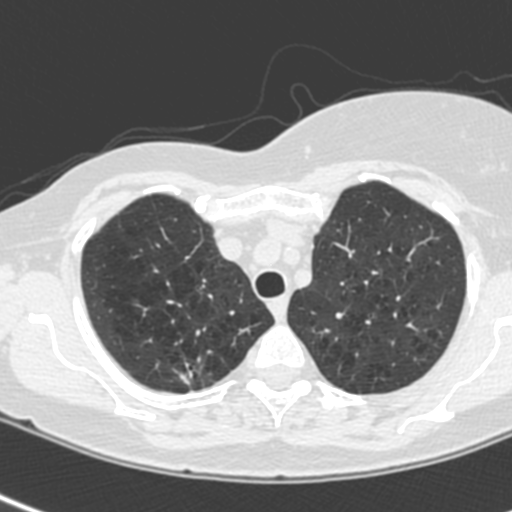
Low-dose screening chest CT, one axial slice. Position 182 of 214 along the scan axis. 120 kVp. Lung window (W 1500 / L -600 HU). 512 × 512 image matrix, field of view 281 × 281 mm.
Annotated regions visible in this slice (manually delineated by an expert):
- lesion 1 (tumor, upper lobe of right lung): bounding box (x1, y1, x2, y2) in pixels: (181, 370, 195, 384)